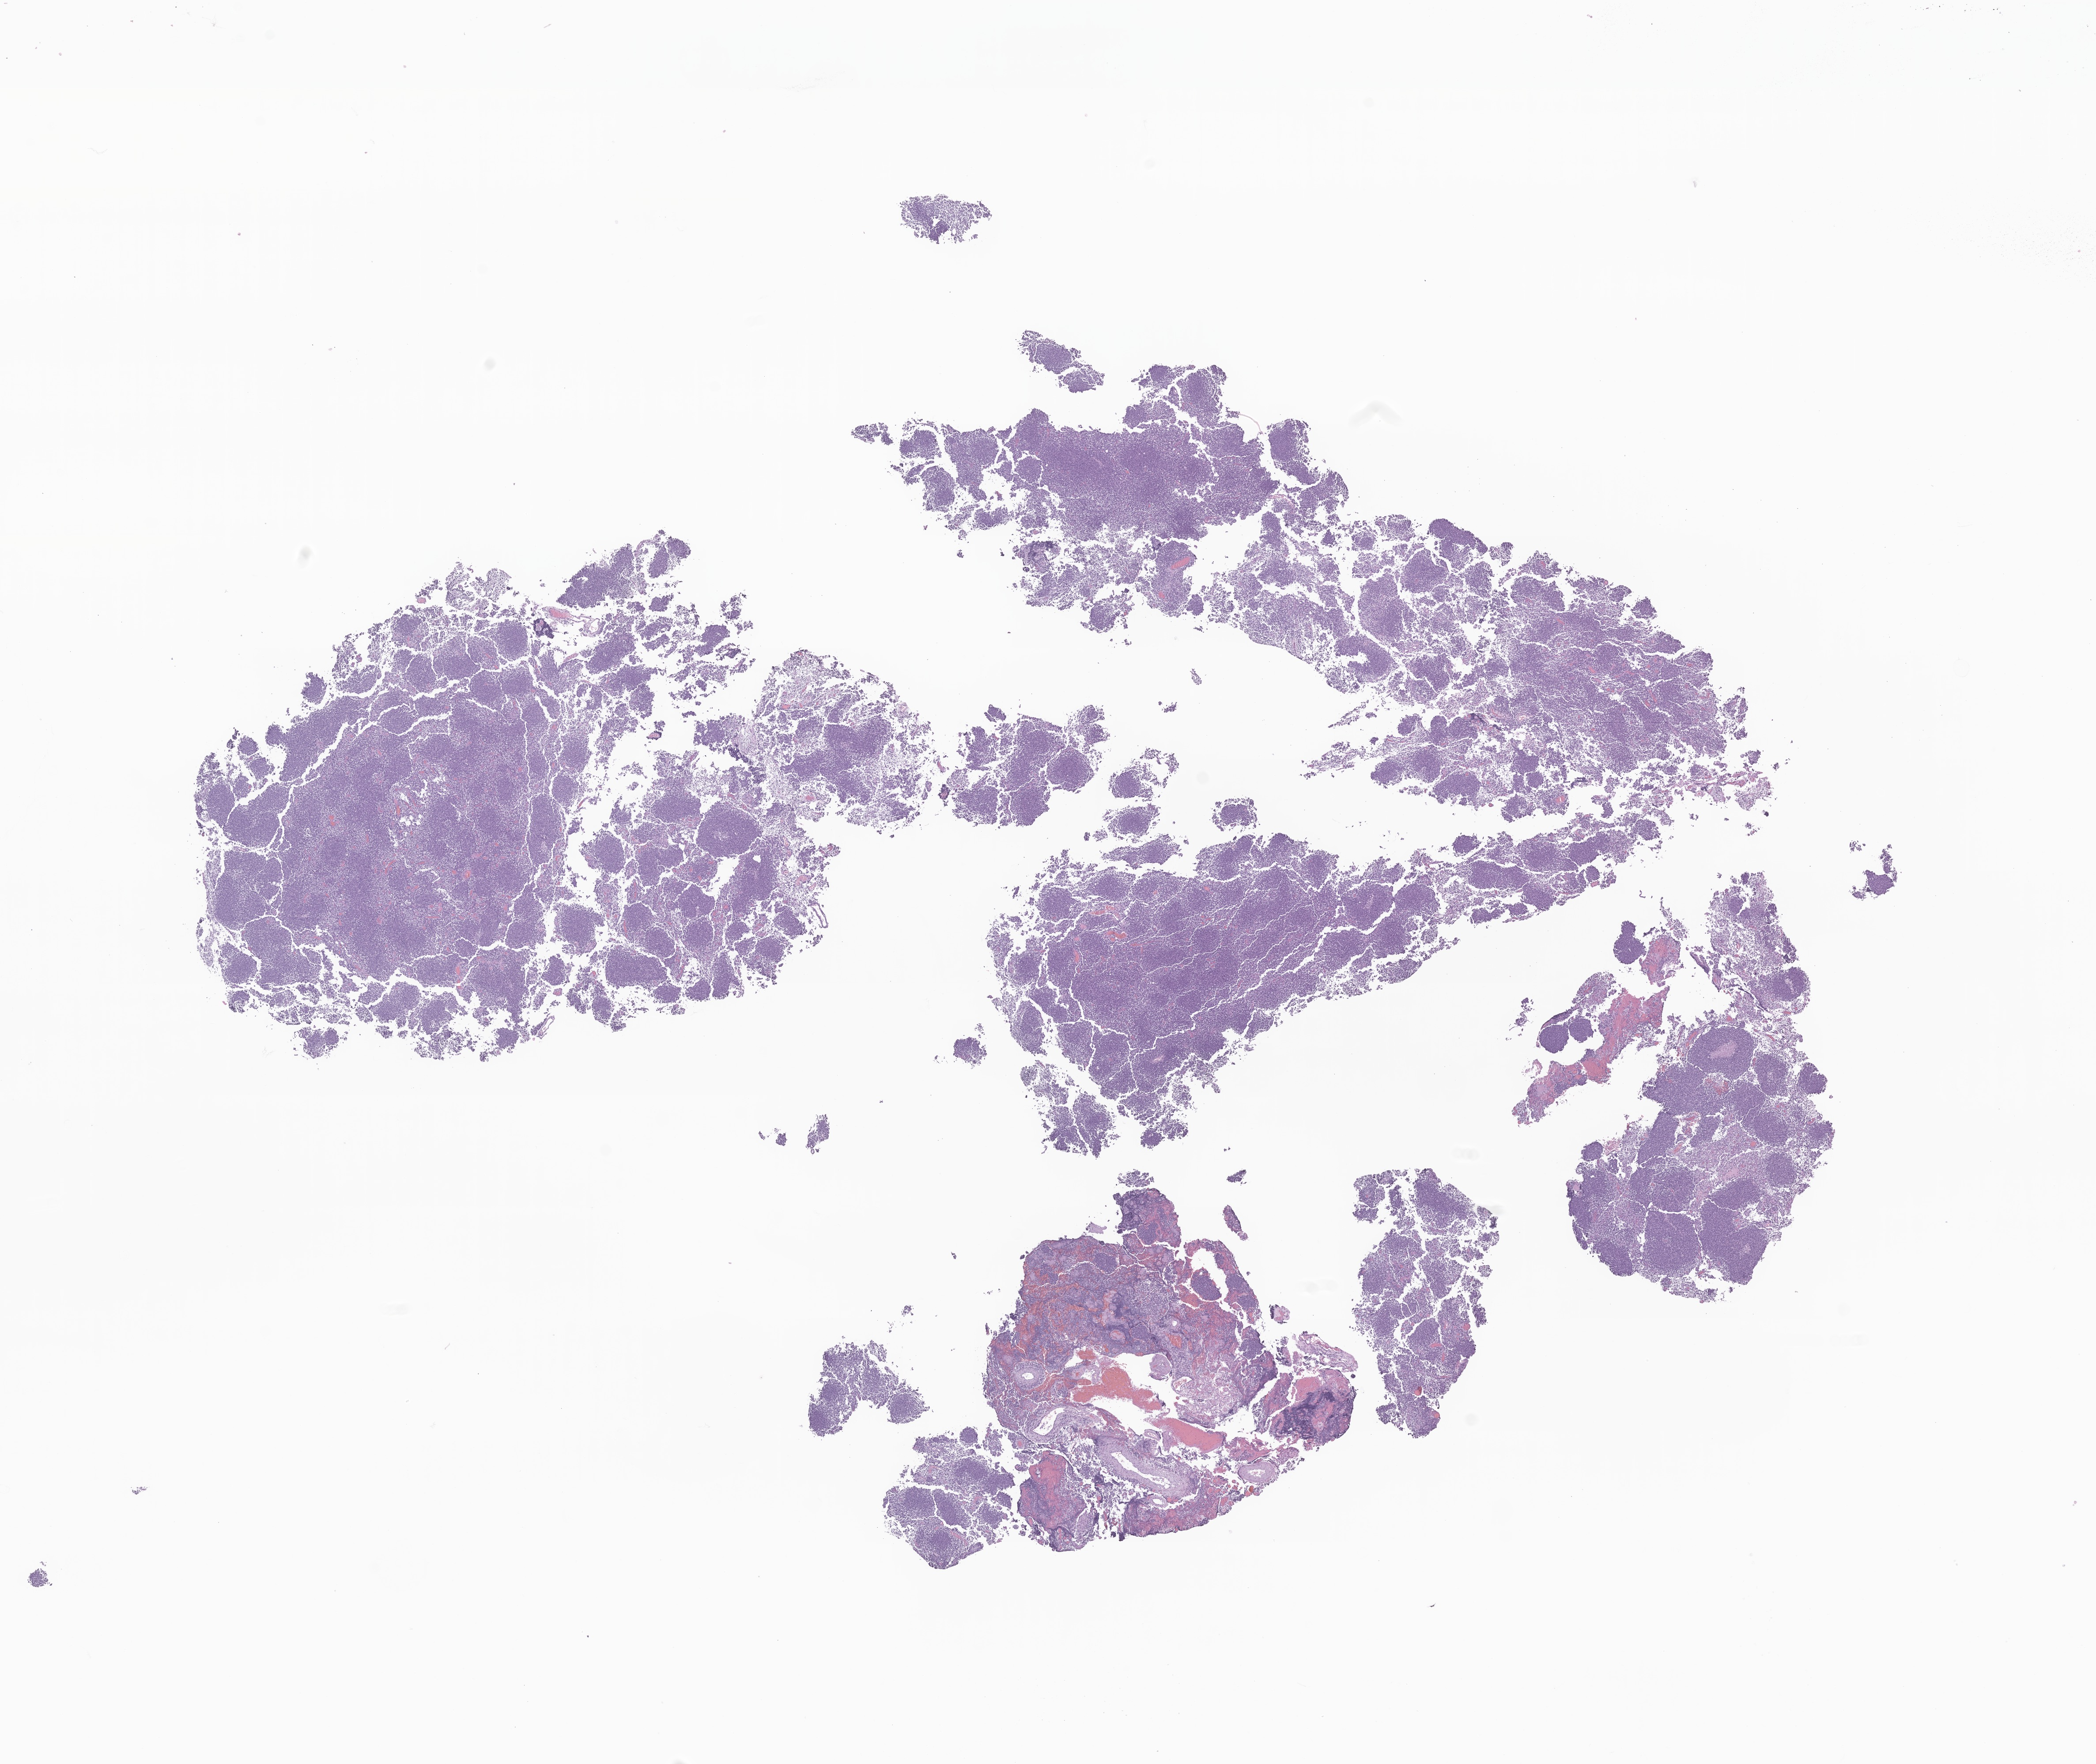
Whole-slide image, H&E stain of tumor tissue from the cerebellum, whole scanned area (about 20.0 x 16.8 mm) shown as a low-resolution overview. Formalin-fixed paraffin-embedded section. Patient male; age 258 months (21 years 6 months).
Recorded diagnosis: Medulloblastoma, NOS.